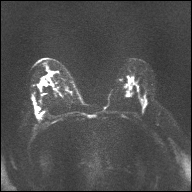
Breast MRI, one axial slice. Position 20 of 32 along the scan axis. Diffusion-weighted series; image 2 of 4 stored at this slice position (different b-values; order by instance number). 1.5 T. 192 × 192 image matrix. Female patient.
Structures marked on this image (outlined manually by an expert reader):
- tumour on diffusion-weighted imaging: bounding box (x1, y1, x2, y2) in pixels: (41, 81, 46, 84)